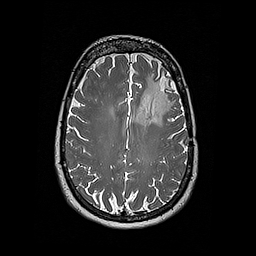
Brain MRI from a brain-tumour surgery series, one axial slice. Position 123 of 192 along the scan axis. 1 mm slice thickness. 256 × 256 image matrix. Case-level facts recorded for this patient, not image findings: histopathology: Oligodendroglioma; WHO grade: 2; IDH mutation: yes; tumour location: Left Frontal.
Structures marked on this image (outlined manually by an expert reader):
- tumour: bounding box [x1, y1, x2, y2] px = [136, 73, 174, 127]